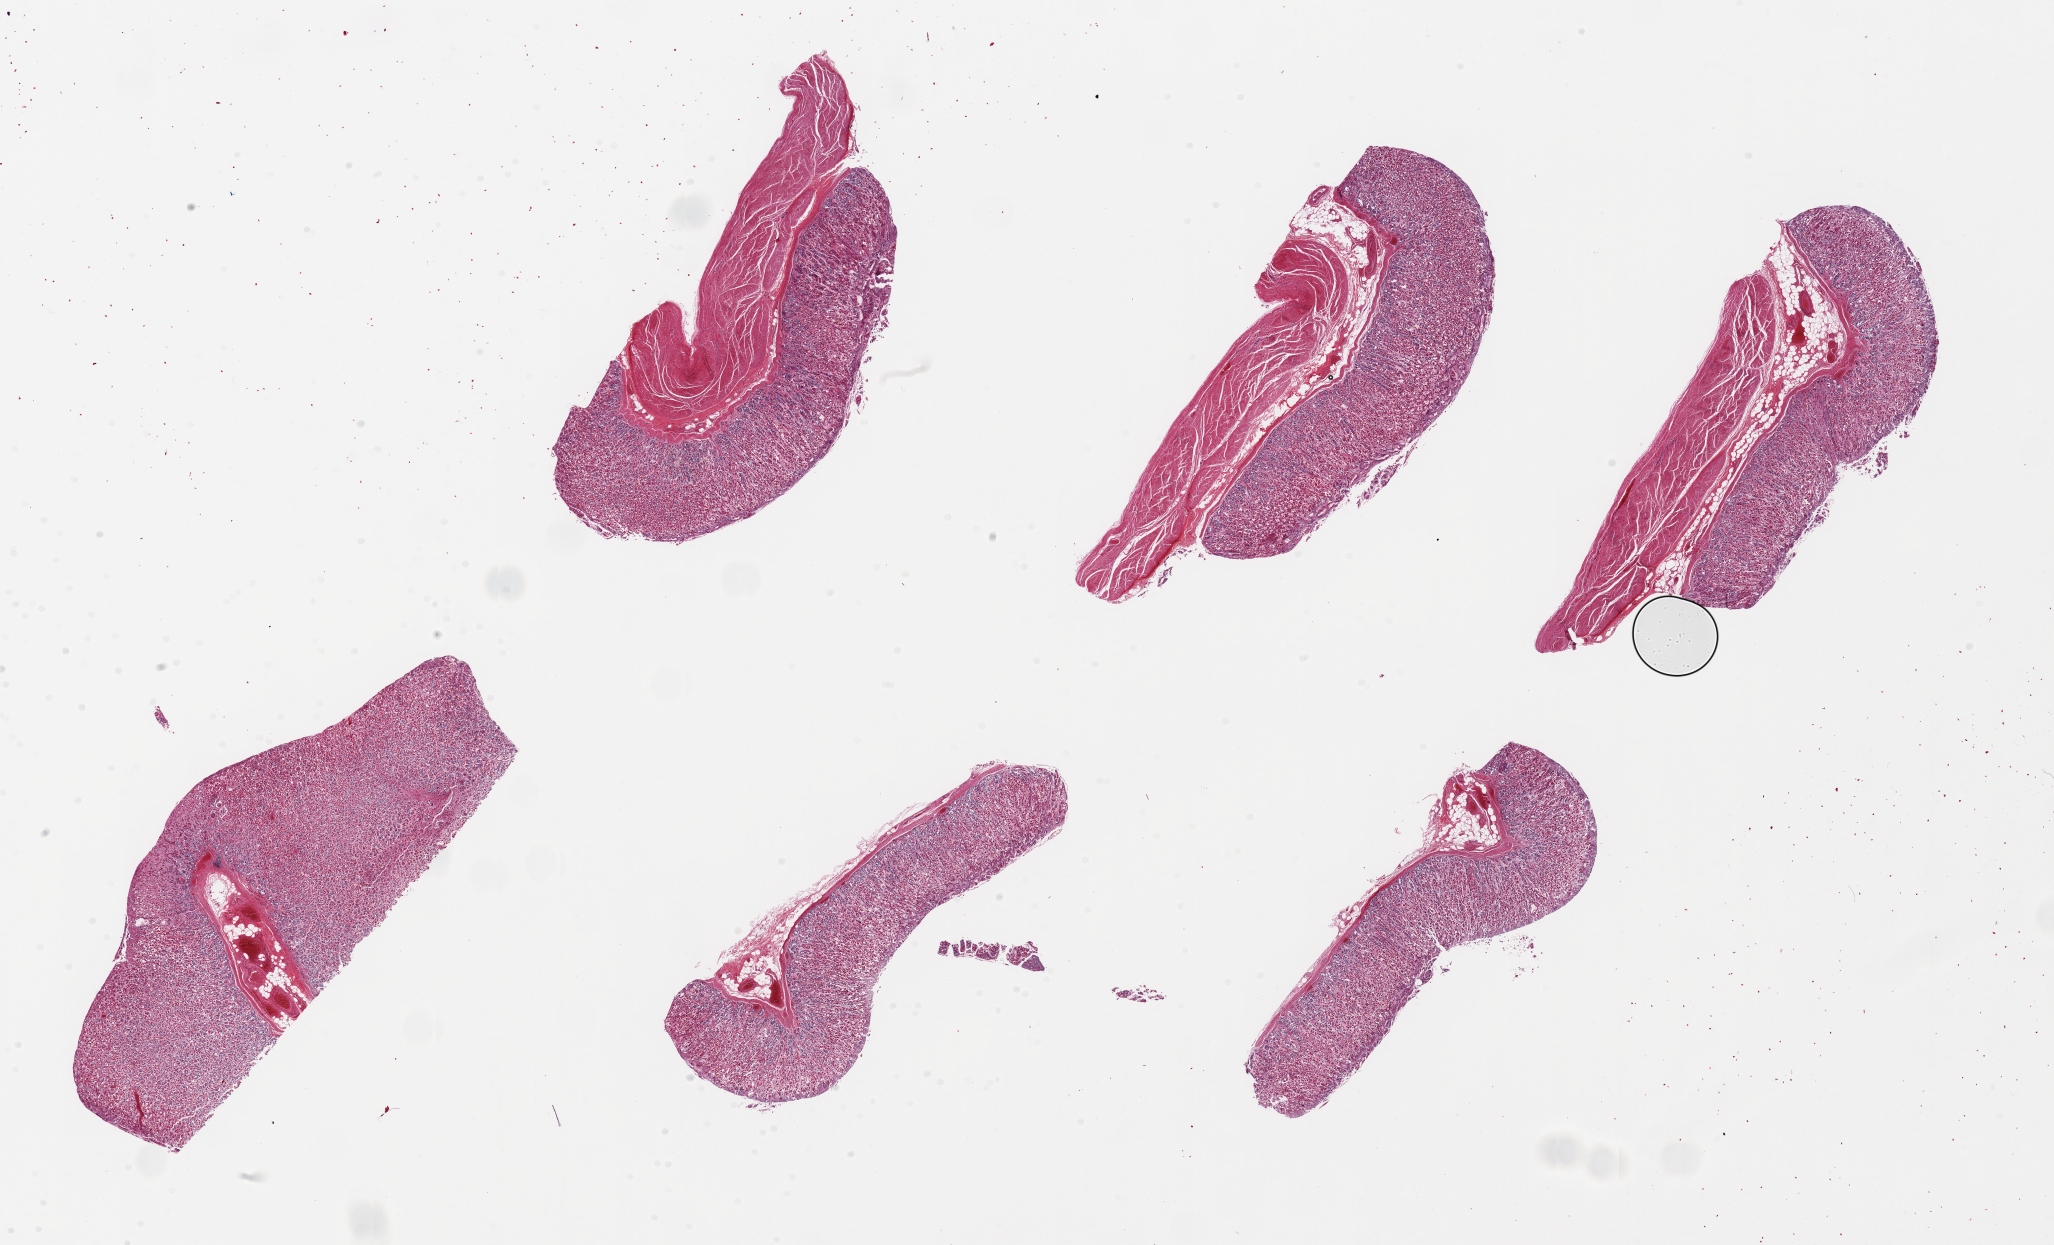
Haematoxylin and eosin whole-slide image, low-resolution overview of the scanned area, about 32.5 x 19.7 mm; PAXgene-fixed paraffin-embedded (PFPE) section; section of stomach (target tissue); tissue donor sample. Donor sex: male.
Pathologist's review note for this sample: 6 pieces ~8x3mm, ~40-50% mucosa, but badly autolyzed.